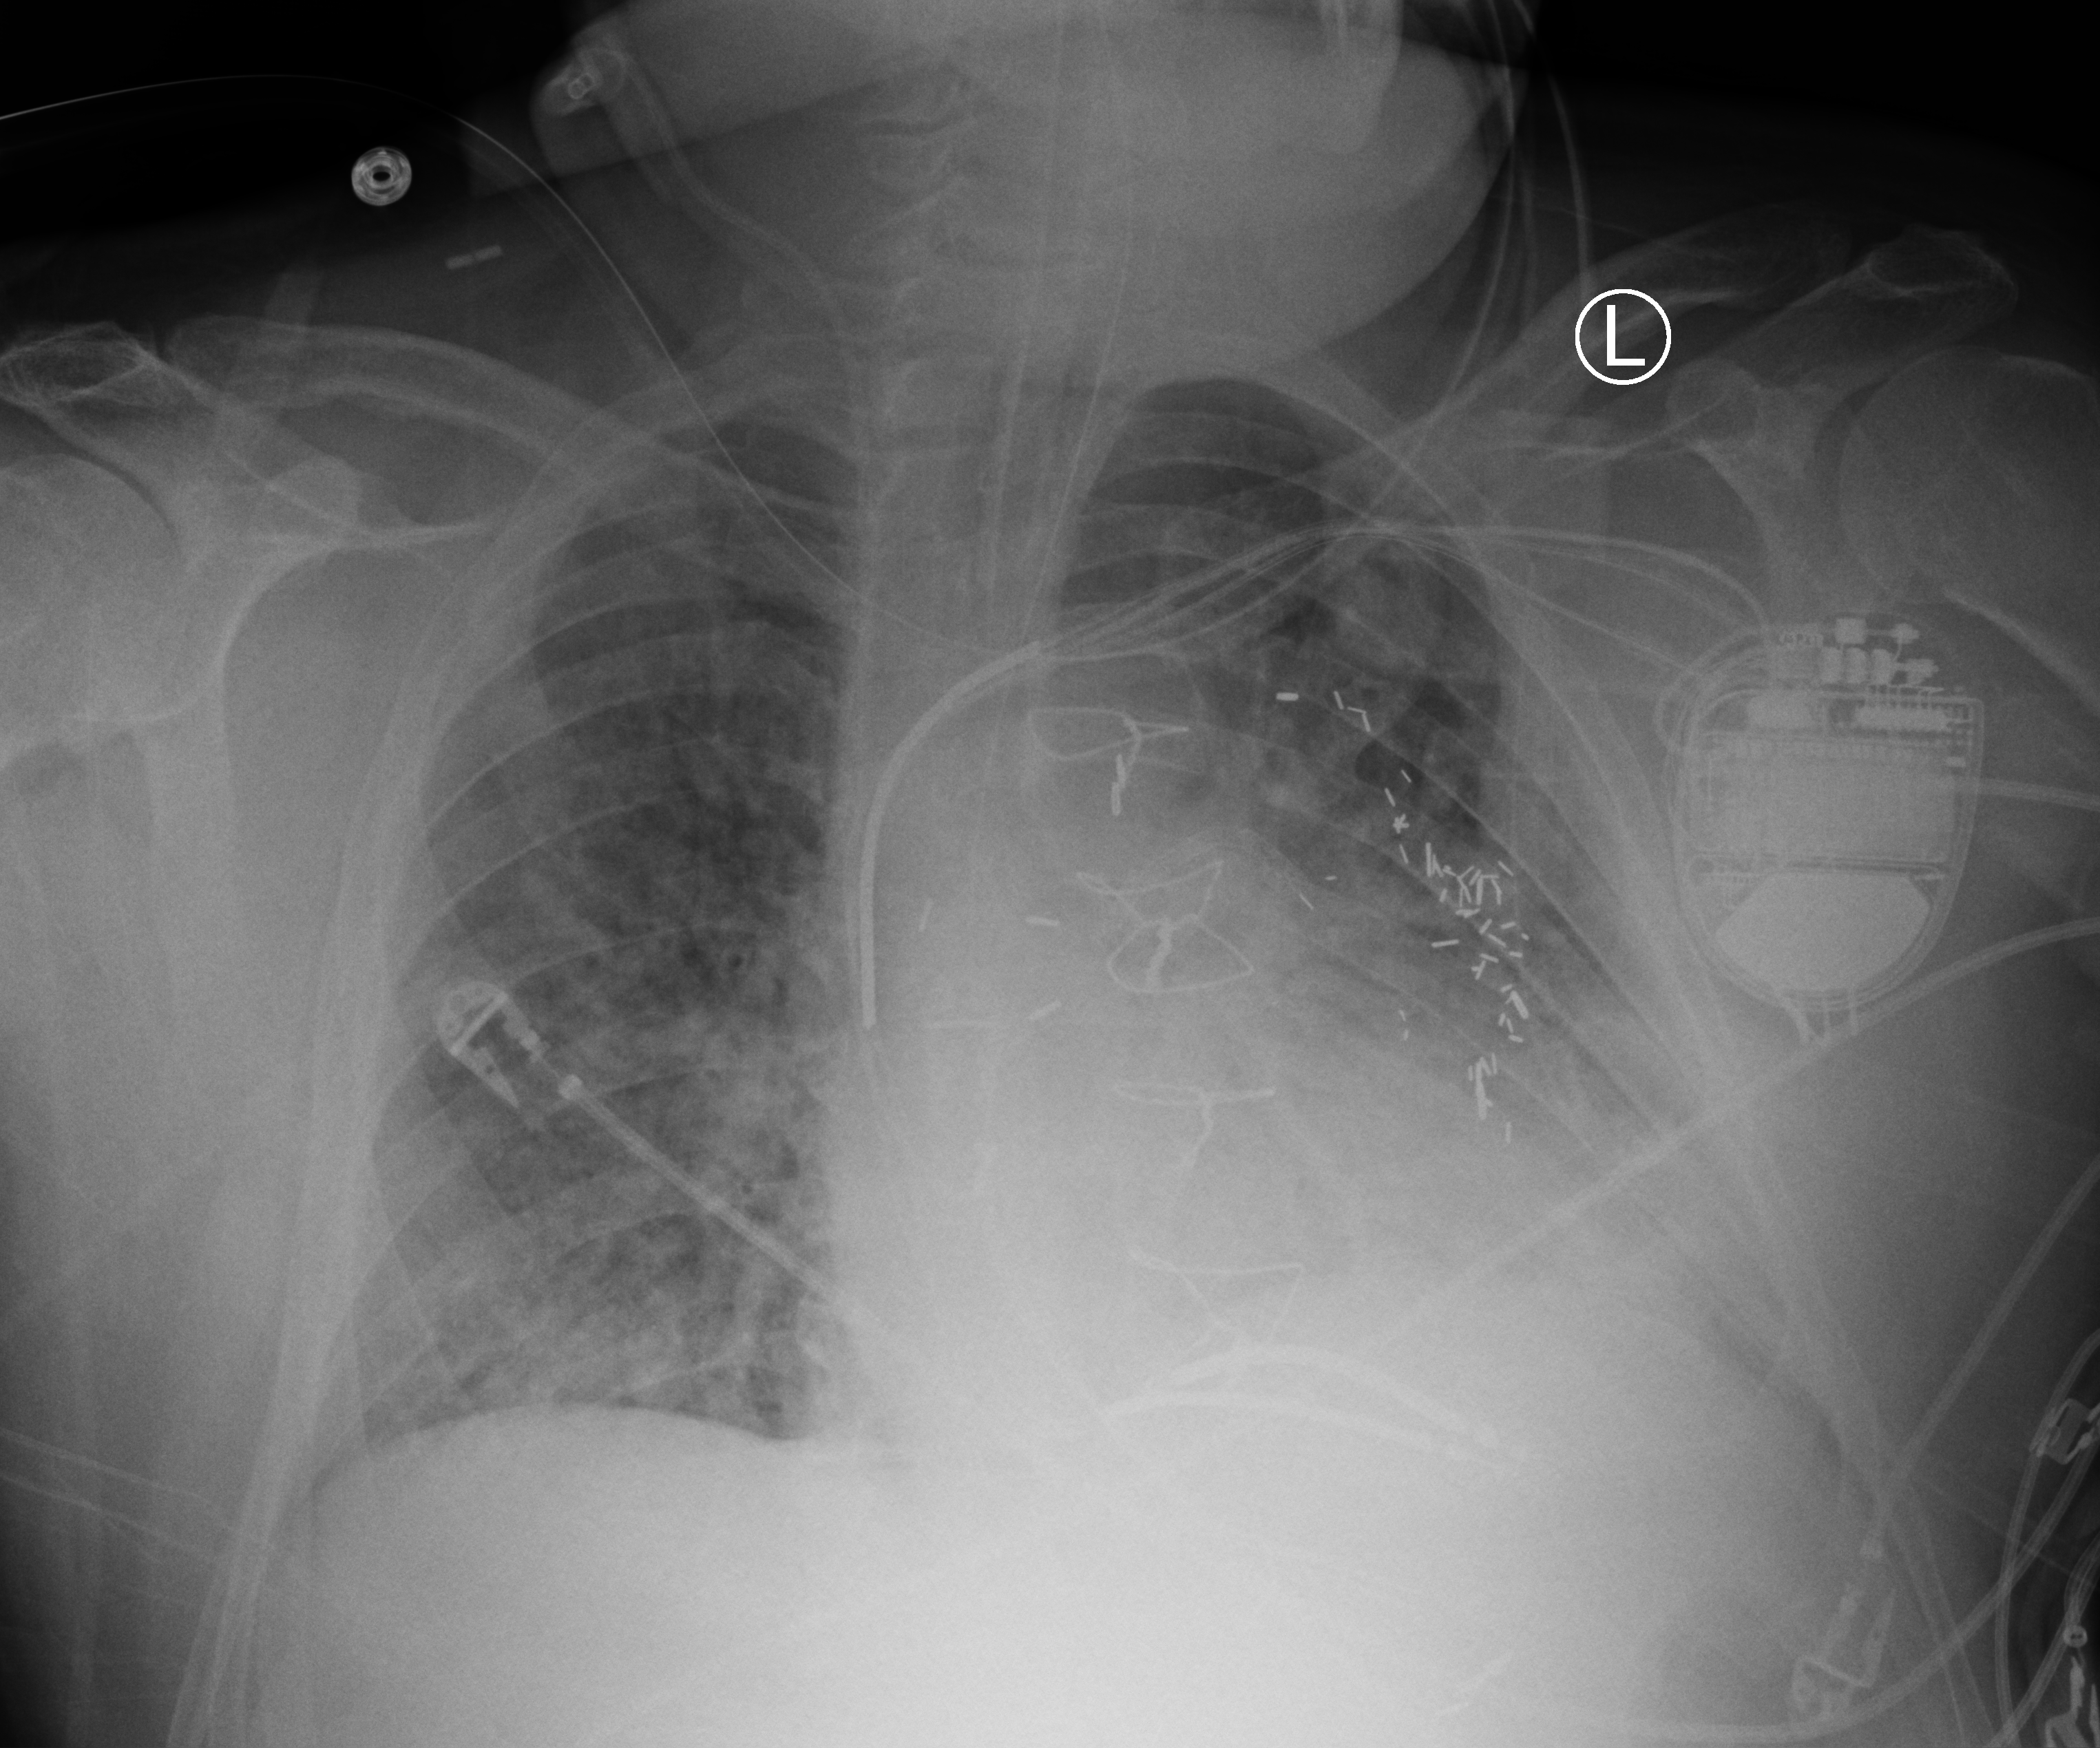
Portable chest radiograph. Male patient hospitalised with COVID-19, age 60–74 years.
Hospital-stay facts (about this admission, not read from this image; timing relative to this image not recorded): chronic kidney disease (admission record): no; COPD (admission record): no.